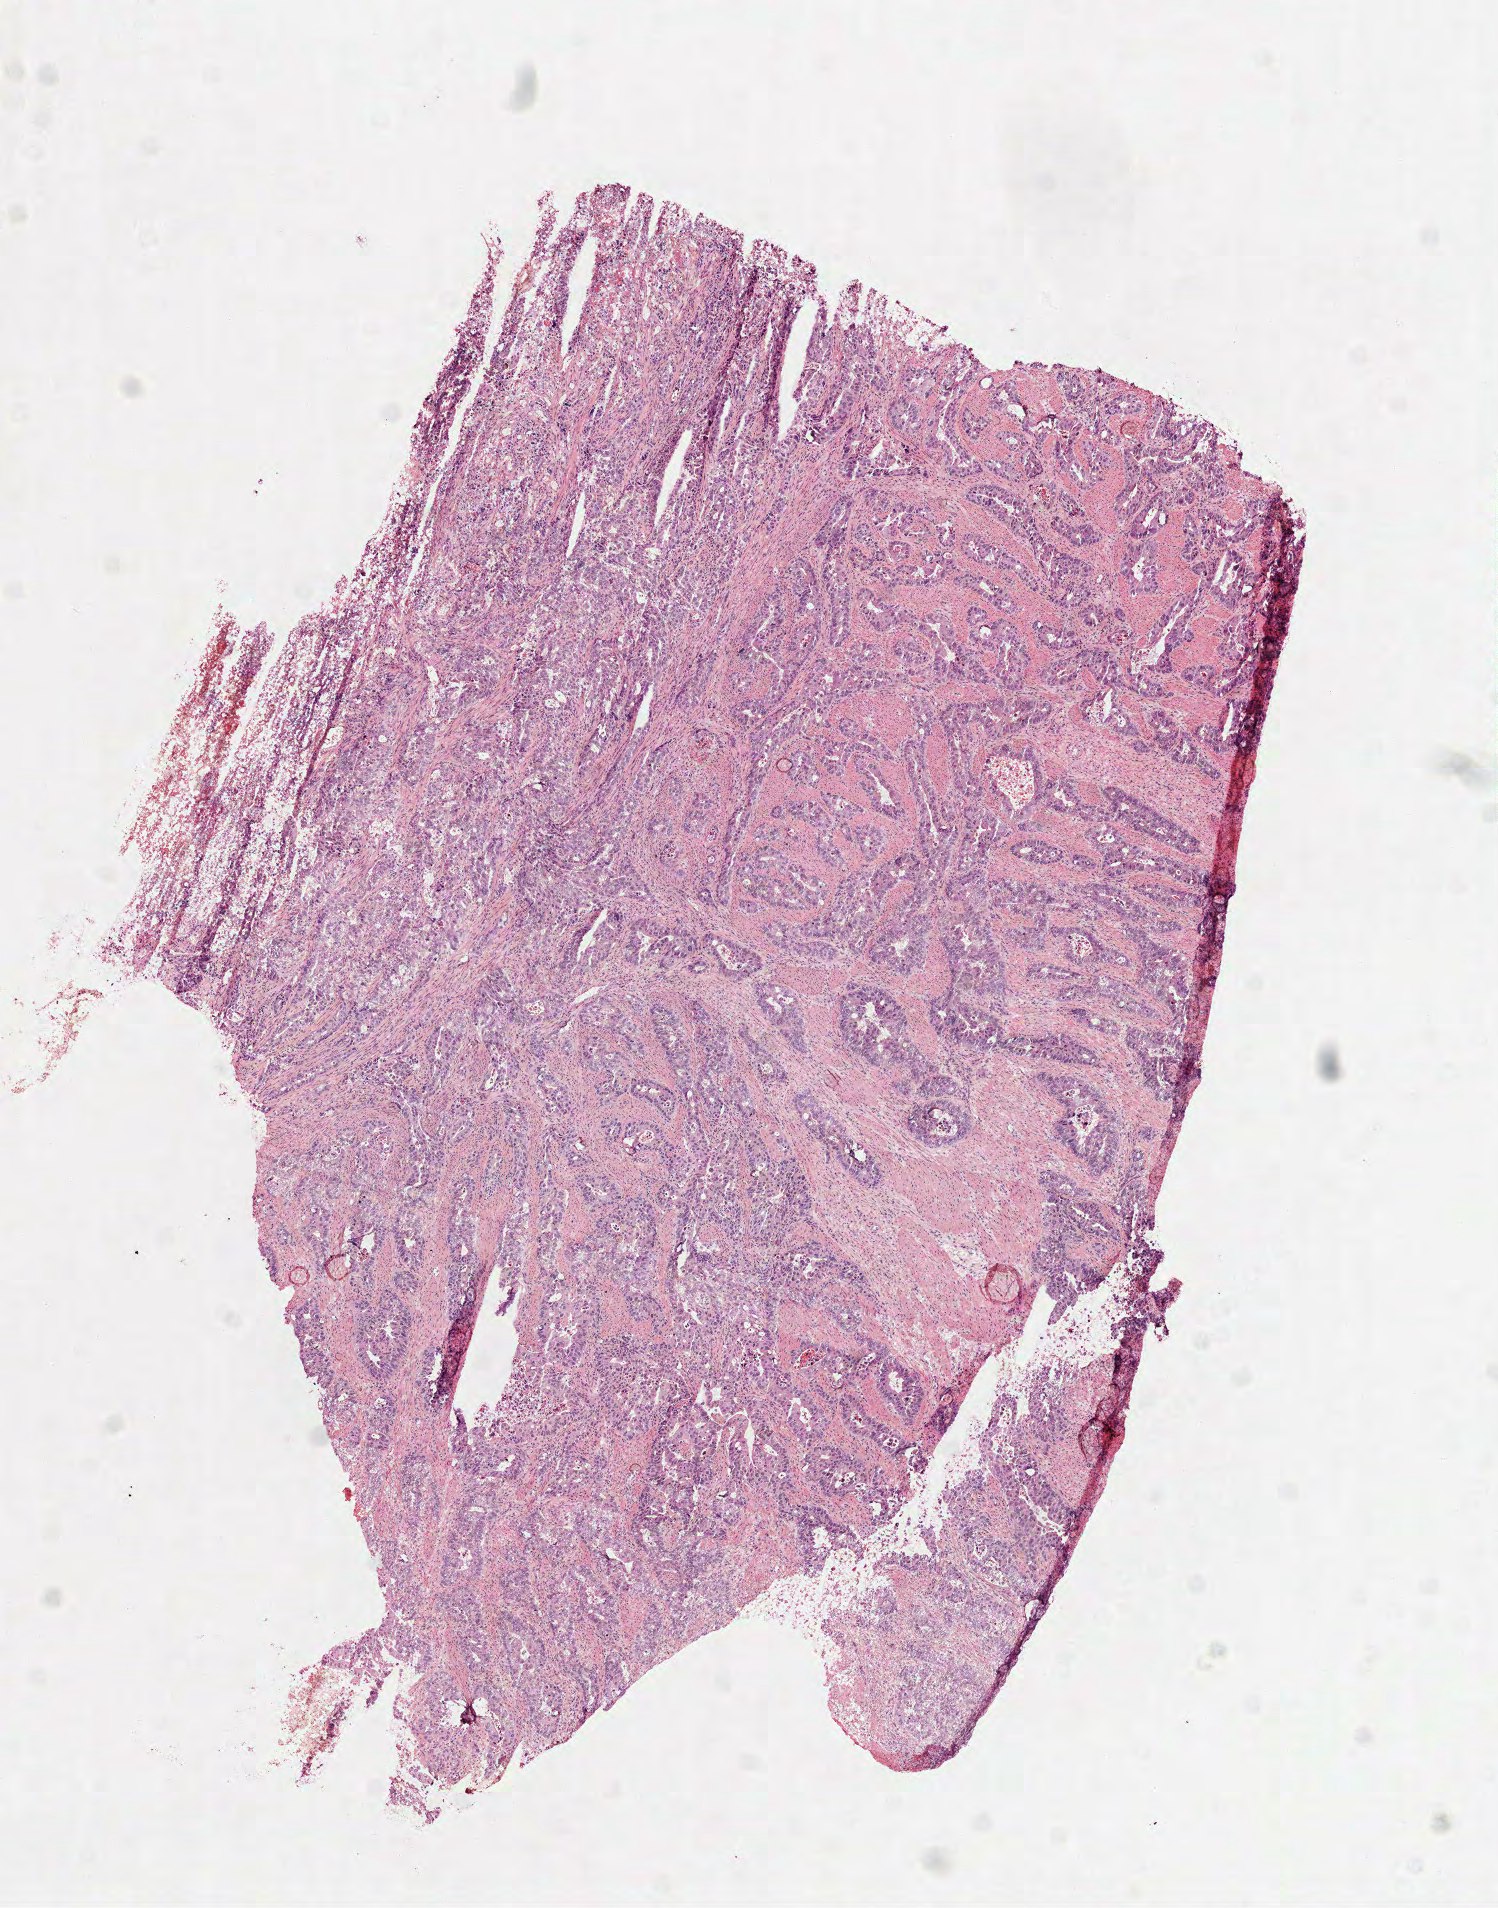
Whole-slide histology image, H&E, a low-resolution overview of the entire scanned area, about 6.0 x 7.7 mm (slide scanned at 40x); frozen section from the top of the tissue portion; stomach, primary tumour sample. Patient: female, age at initial diagnosis 67 years. Histologic grade: G2 (moderately differentiated). Slide review estimates, as recorded: tumour cells 75%, tumour nuclei 75%, normal cells 0%, stromal cells 20%, necrosis 5%.
- lymph nodes positive (case pathology): 3 of 19 examined
- AJCC pathologic stage: IIIA (7th edition)
- TNM: T3 N2 M0
- histologic diagnosis: Tubular adenocarcinoma (body of stomach)